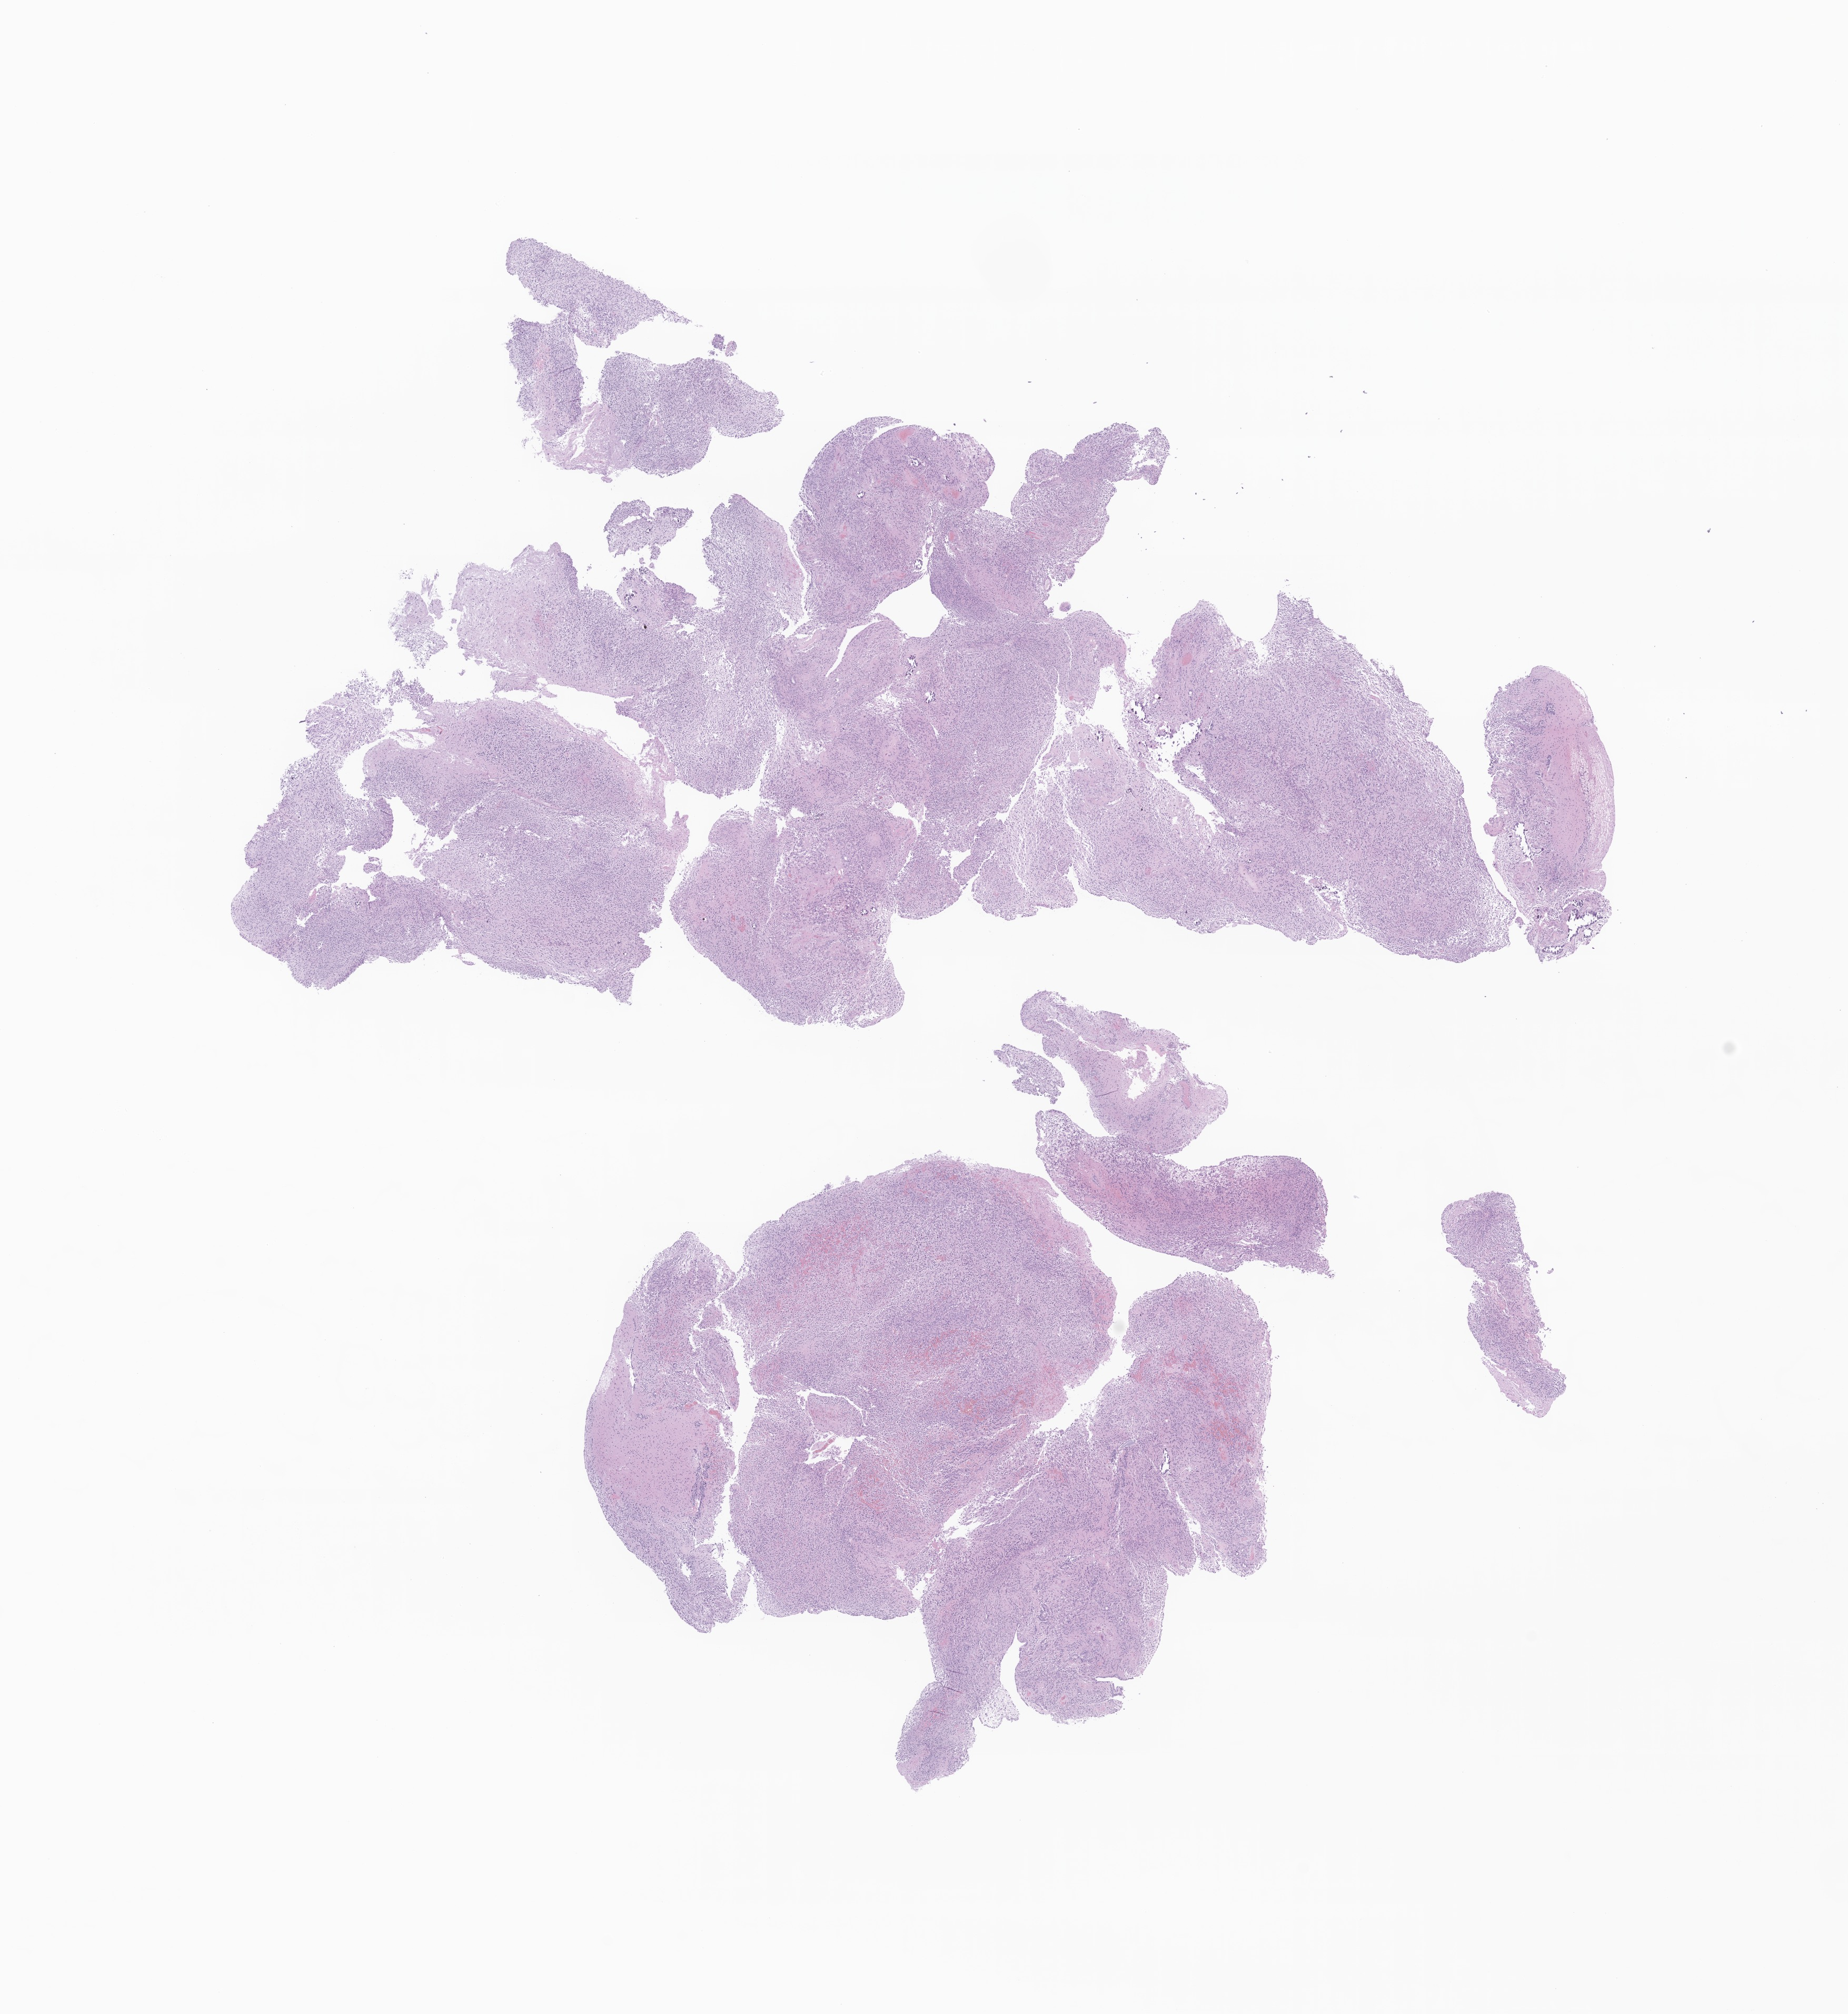
Hematoxylin and eosin (H&E) whole-slide image of tumor tissue from the spinal cord — a low-resolution overview of the entire scanned area, about 14.8 x 16.1 mm, formalin-fixed paraffin-embedded section. Patient: female, age 135 months (11 years 3 months).
Recorded diagnosis: Ependymoma, NOS.